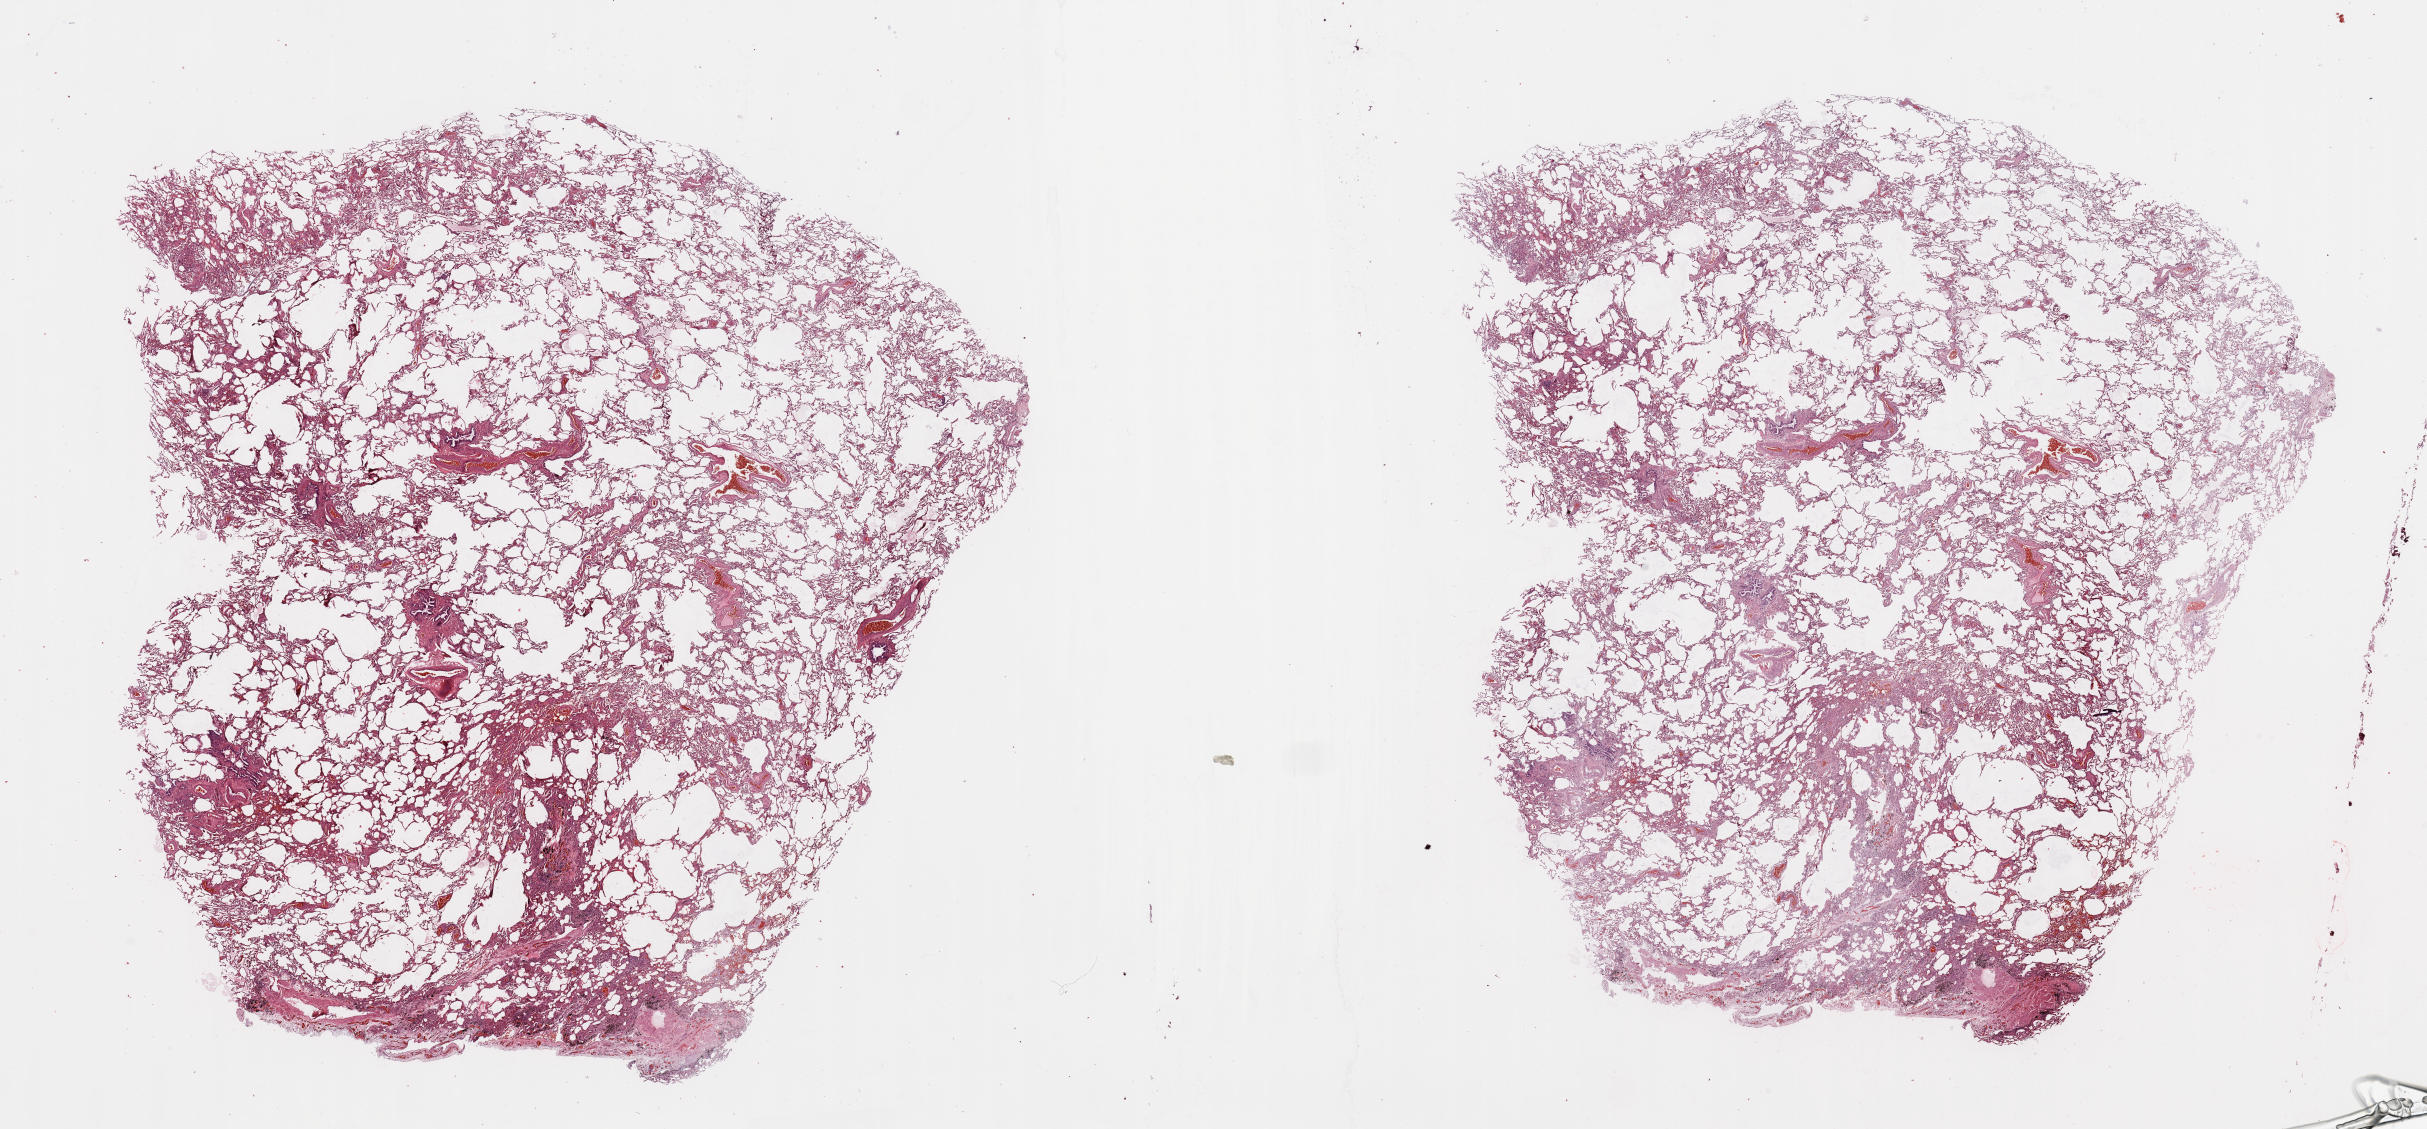
Hematoxylin and eosin (H&E) stained whole-slide image — low-resolution overview of the scanned area, about 38.4 x 17.9 mm (slide scanned at 20x). Lung, normal (non-tumour) tissue. 68-year-old male patient.
This section: normal (non-tumour) tissue from the same patient. Patient diagnosis (cohort enrolment): squamous cell carcinoma (lung).